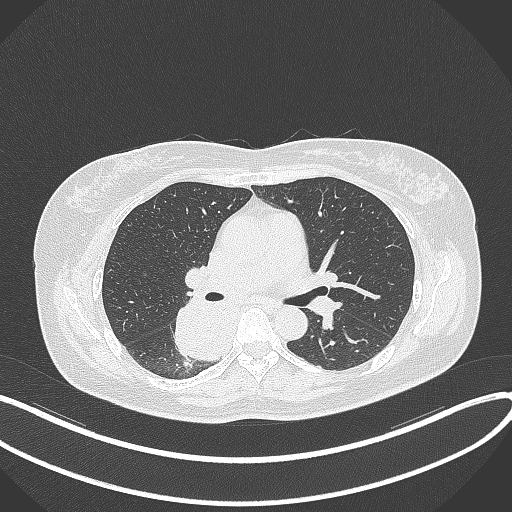
Chest CT, one axial slice. Position 211 of 331 along the scan axis. 120 kVp. Lung window (W 1500 / L -600 HU). 1 mm slice thickness. 512 × 512 image matrix, field of view 400 × 400 mm. Female patient, age 54 years. Case-level facts recorded for this patient, not image findings: clinical TNM (as recorded): T4 N0 M0.
Outlined on this slice (bounding box drawn by a radiologist):
- lung tumour (recorded histology: adenocarcinoma): bounding box (x1, y1, x2, y2) in pixels: (171, 299, 227, 362)